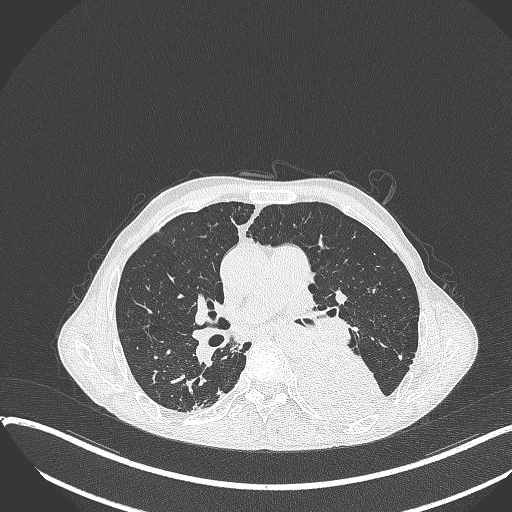
Chest CT, one axial slice; slice 211 of 401 in the series (ordered by position); reconstruction kernel B70f; 120 kVp; lung window (W 1500 / L -600 HU); 512 × 512 image matrix, field of view 400 × 400 mm. Male patient, age 57 years. From the clinical record (not read from this slice): clinical TNM (as recorded): T4 N0 M0.
Outlined on this slice (bounding box drawn by a radiologist):
- lung tumour (recorded histology: squamous cell carcinoma): box from (x=293, y=351) to (x=387, y=424) px